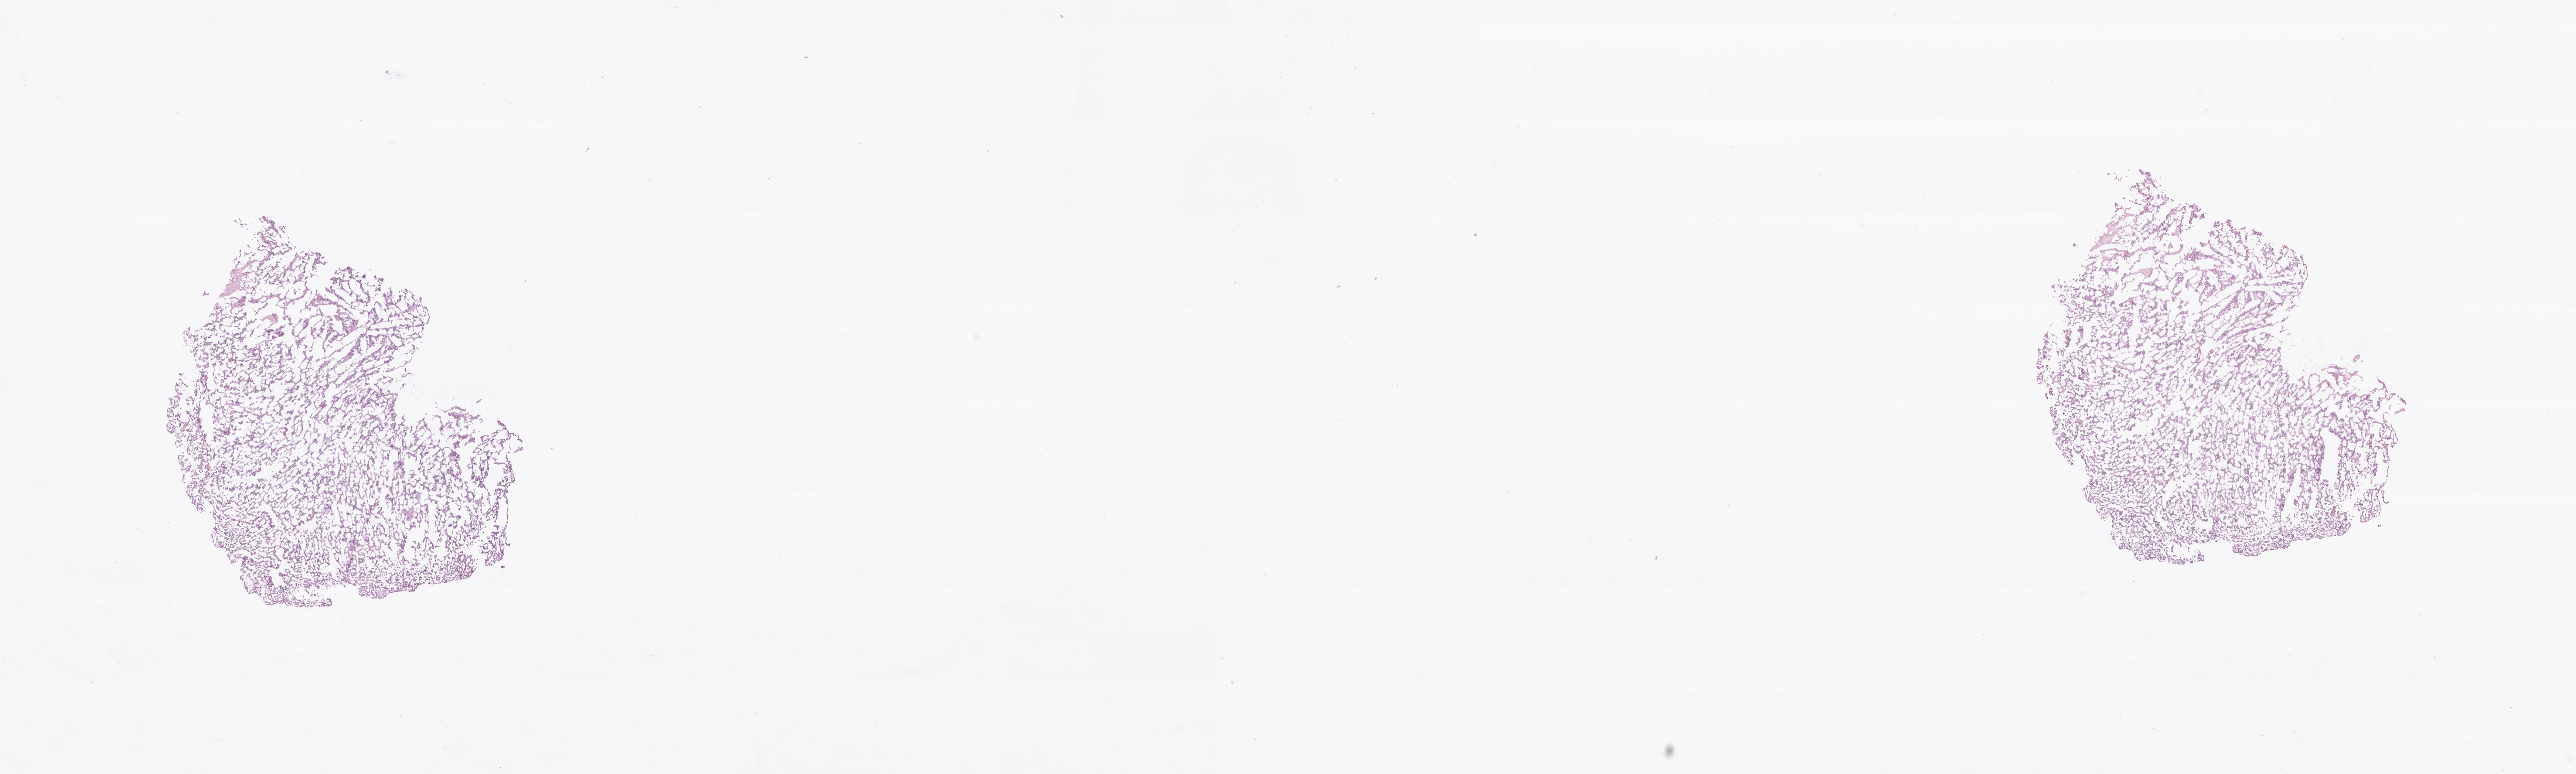
Hematoxylin and eosin (H&E) whole-slide image of tumor tissue from the parietal lobe, a low-resolution overview of the entire scanned area, about 29.3 x 8.8 mm. Frozen section. Patient: female, age 160 months (13 years 4 months).
* recorded diagnosis: Astroblastoma